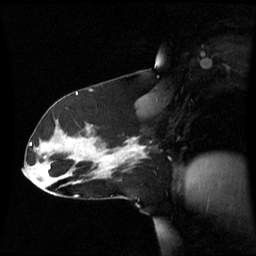
Breast MRI (dynamic contrast-enhanced), one sagittal slice. Slice 35 of 60 in the series (ordered by position). Dynamic contrast-enhanced series, image 2 of 3 at this slice position (ordered by acquisition). 1.5 T. TE 4.2 ms, TR 8.4 ms. 256 × 256 image matrix, field of view 270 × 270 mm. Patient: female, 39 years. Case-level facts recorded for this patient, not image findings: setting: breast cancer imaged before/during neoadjuvant chemotherapy; receptor status: triple-negative.
Outlined on this slice (semi-automatic segmentation, software-assisted and operator-edited):
- analysis volume of interest (the breast-tissue region the enhancement analysis was run in; not a lesion): bounding box [x1, y1, x2, y2] px = [101, 137, 146, 173]
- tumour enhancement mask (voxels above the 70 % enhancement threshold inside the analysis volume of interest): [101, 146, 144, 160]